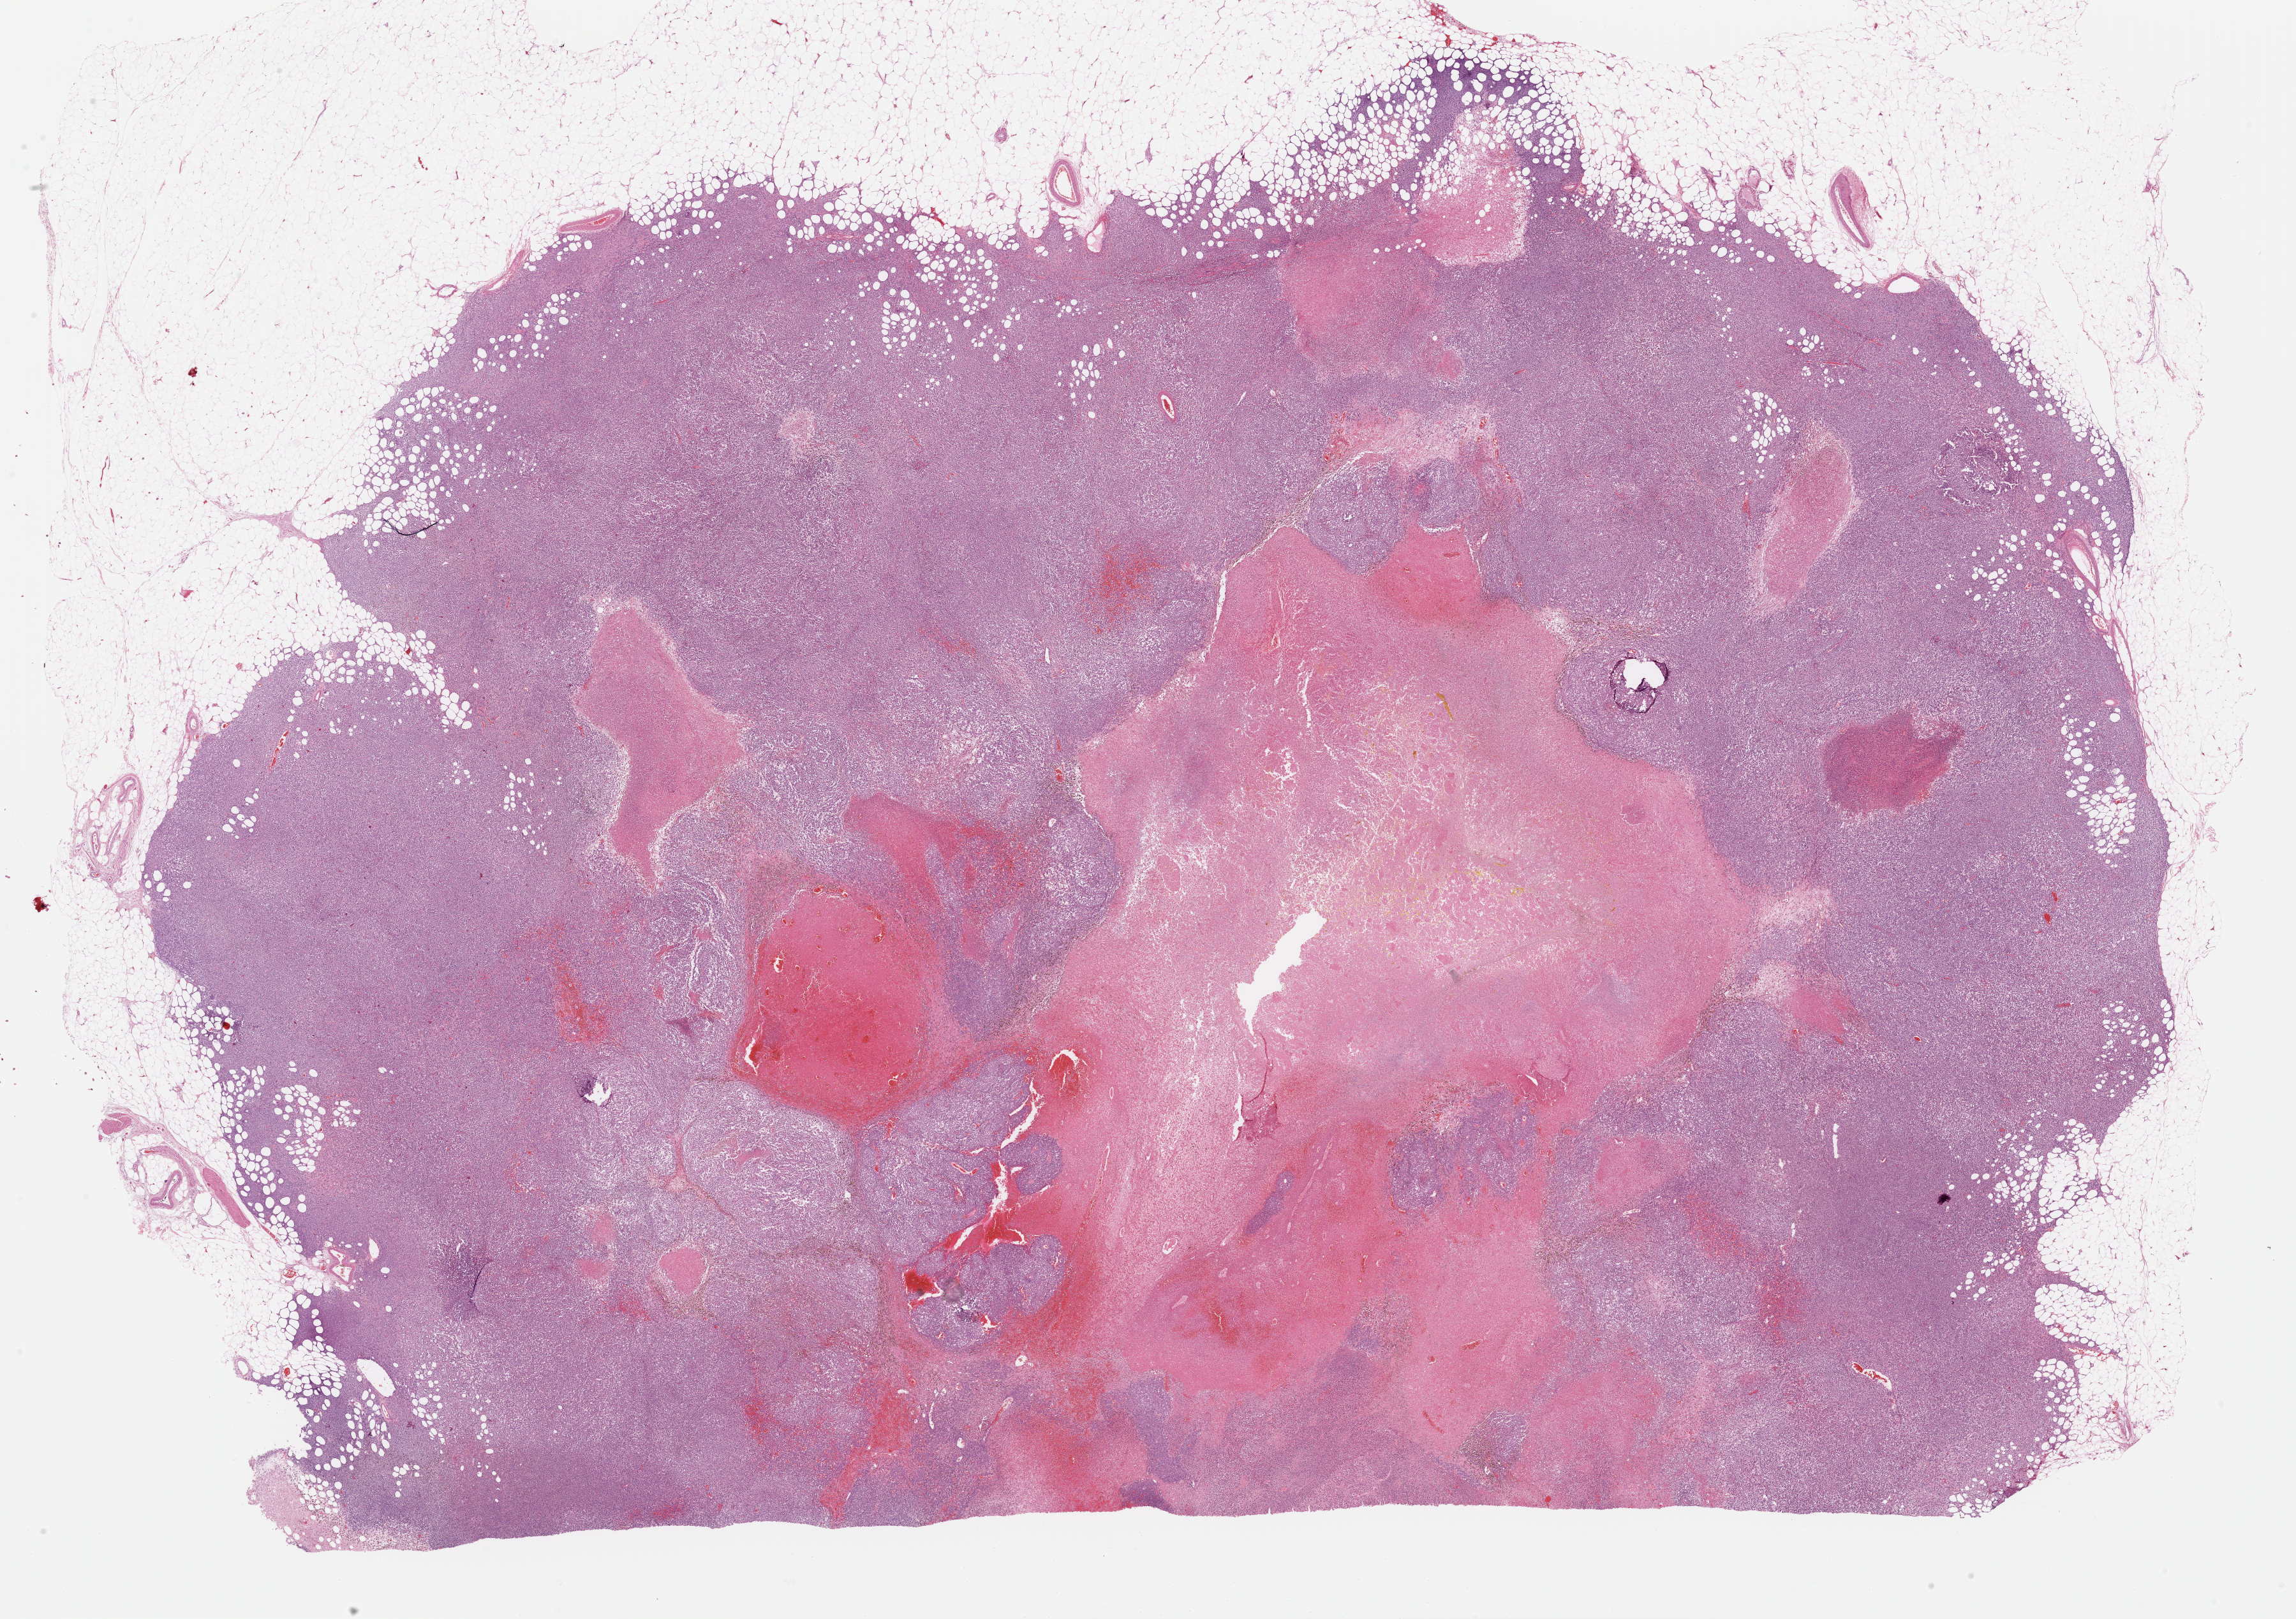
Hematoxylin and eosin (H&E) stained whole-slide image, shown as a low-resolution overview of the whole scanned area (about 28.4 x 20.0 mm, from a 40x scan). Formalin-fixed paraffin-embedded (FFPE) diagnostic section. Primary tumour sample from the skin. Patient: male, age at initial diagnosis 39 years.
Histologic diagnosis: Malignant melanoma, NOS.